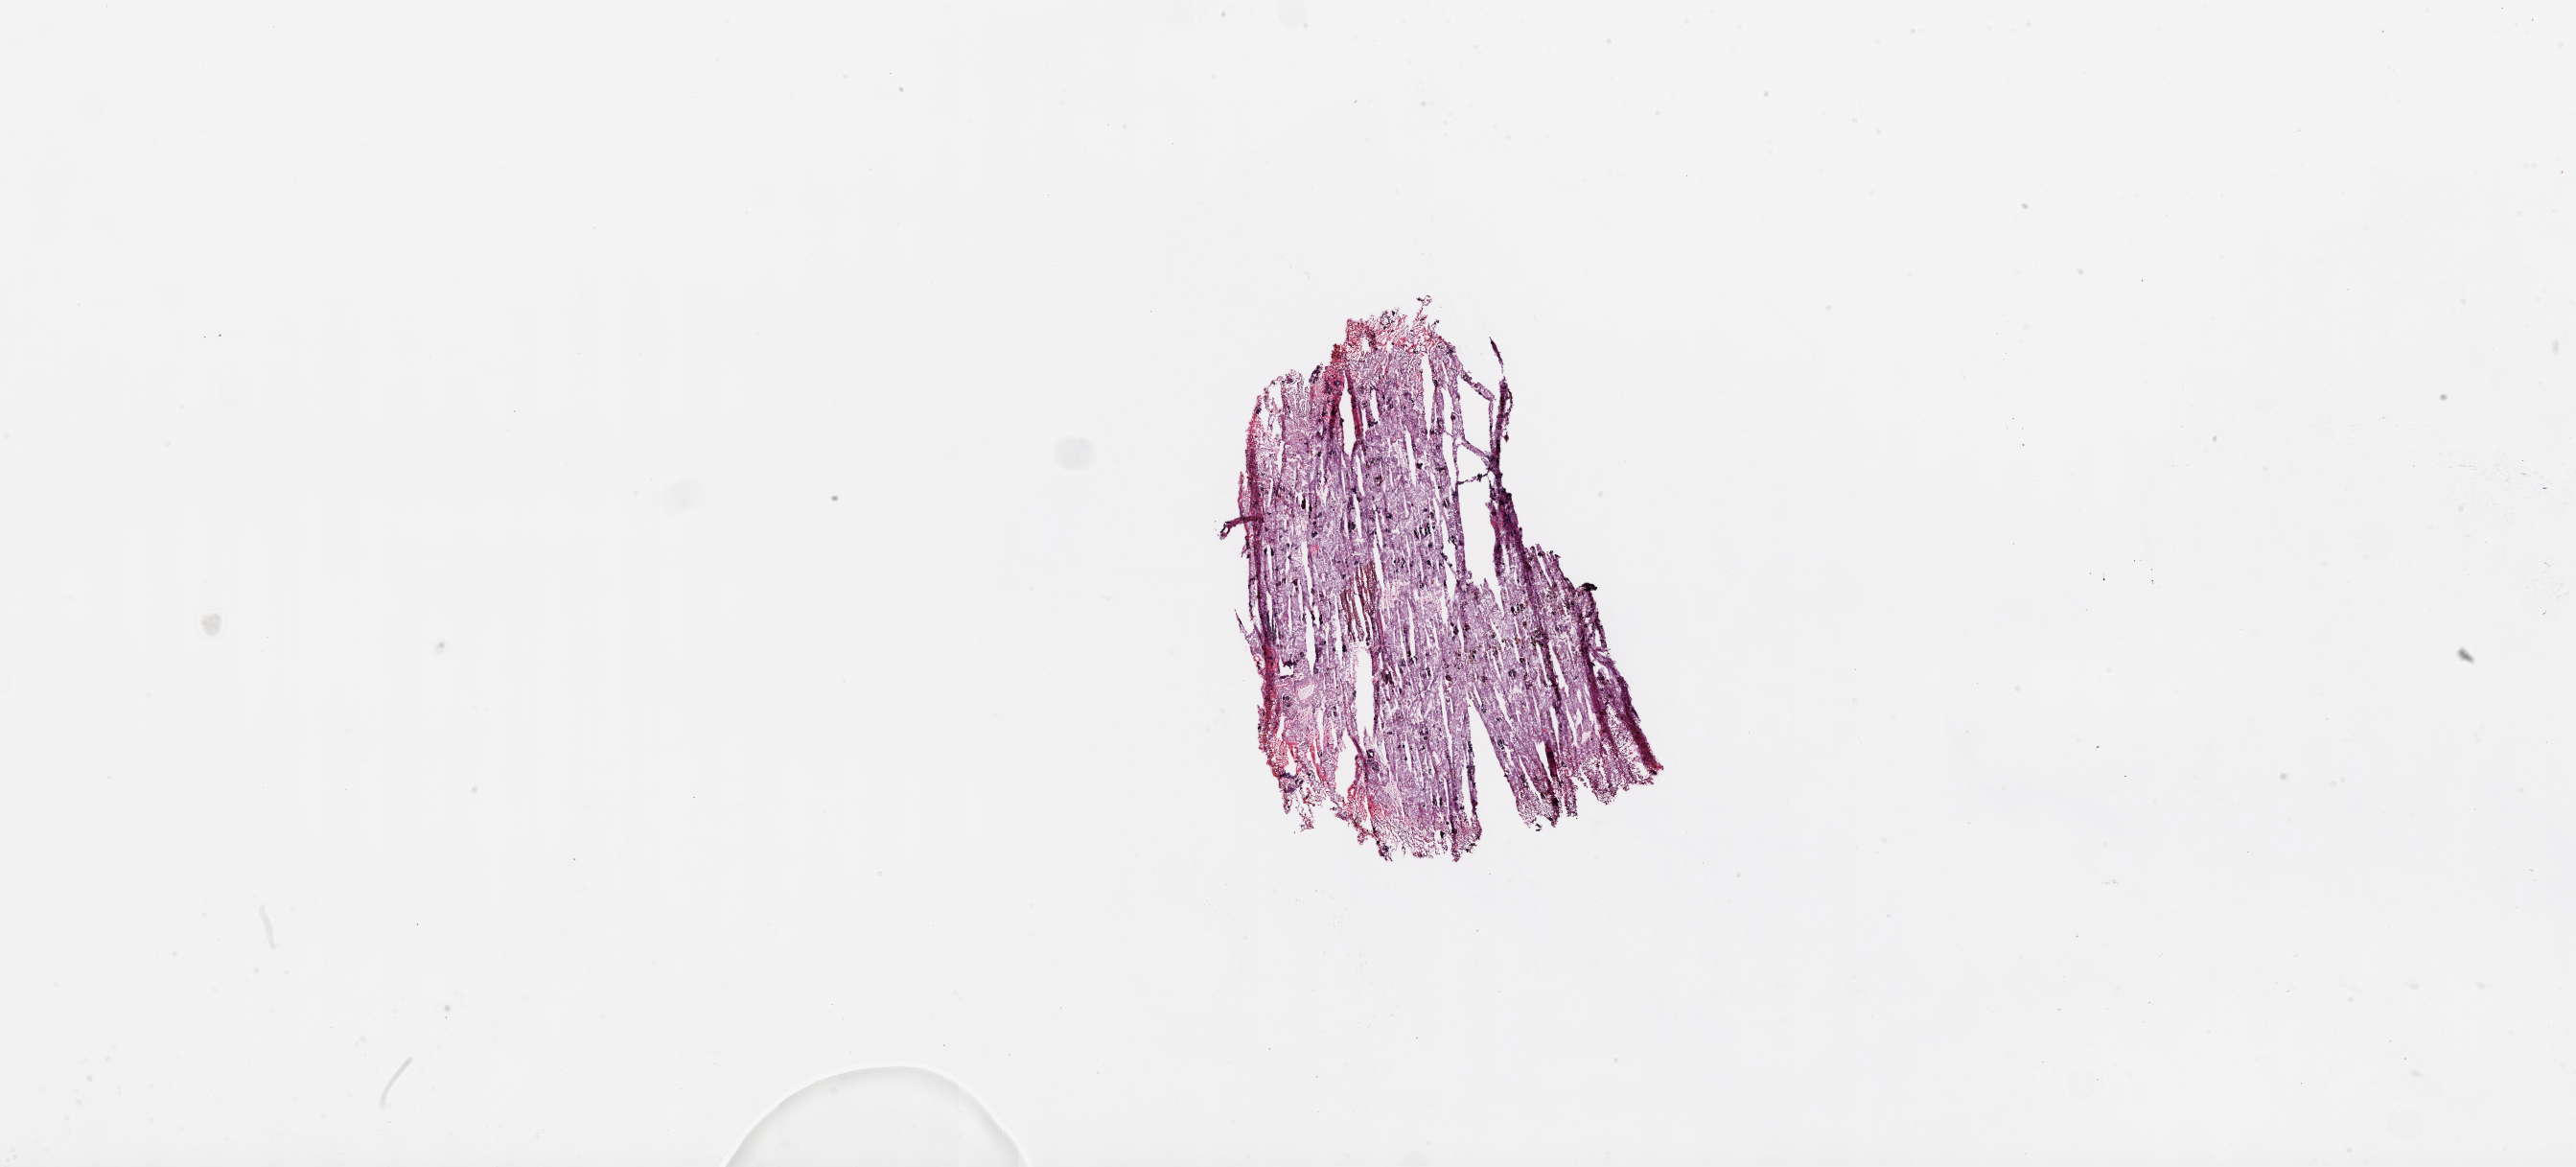
Digitized H&E tissue section (whole slide) — whole scanned area (about 43.1 x 19.5 mm, slide scanned at 20x) shown as a low-resolution overview. Frozen section. Kidney, primary tumour sample. Female, age 51 years at initial diagnosis. Histologic grade: G2 (moderately differentiated). Composition of this section per pathologist review: tumour cells 95%, tumour nuclei 80%, normal cells 0%, stromal cells 5%, necrosis 0%.
Laterality: right. AJCC pathologic stage: I. Diagnosis: Clear cell adenocarcinoma, NOS.